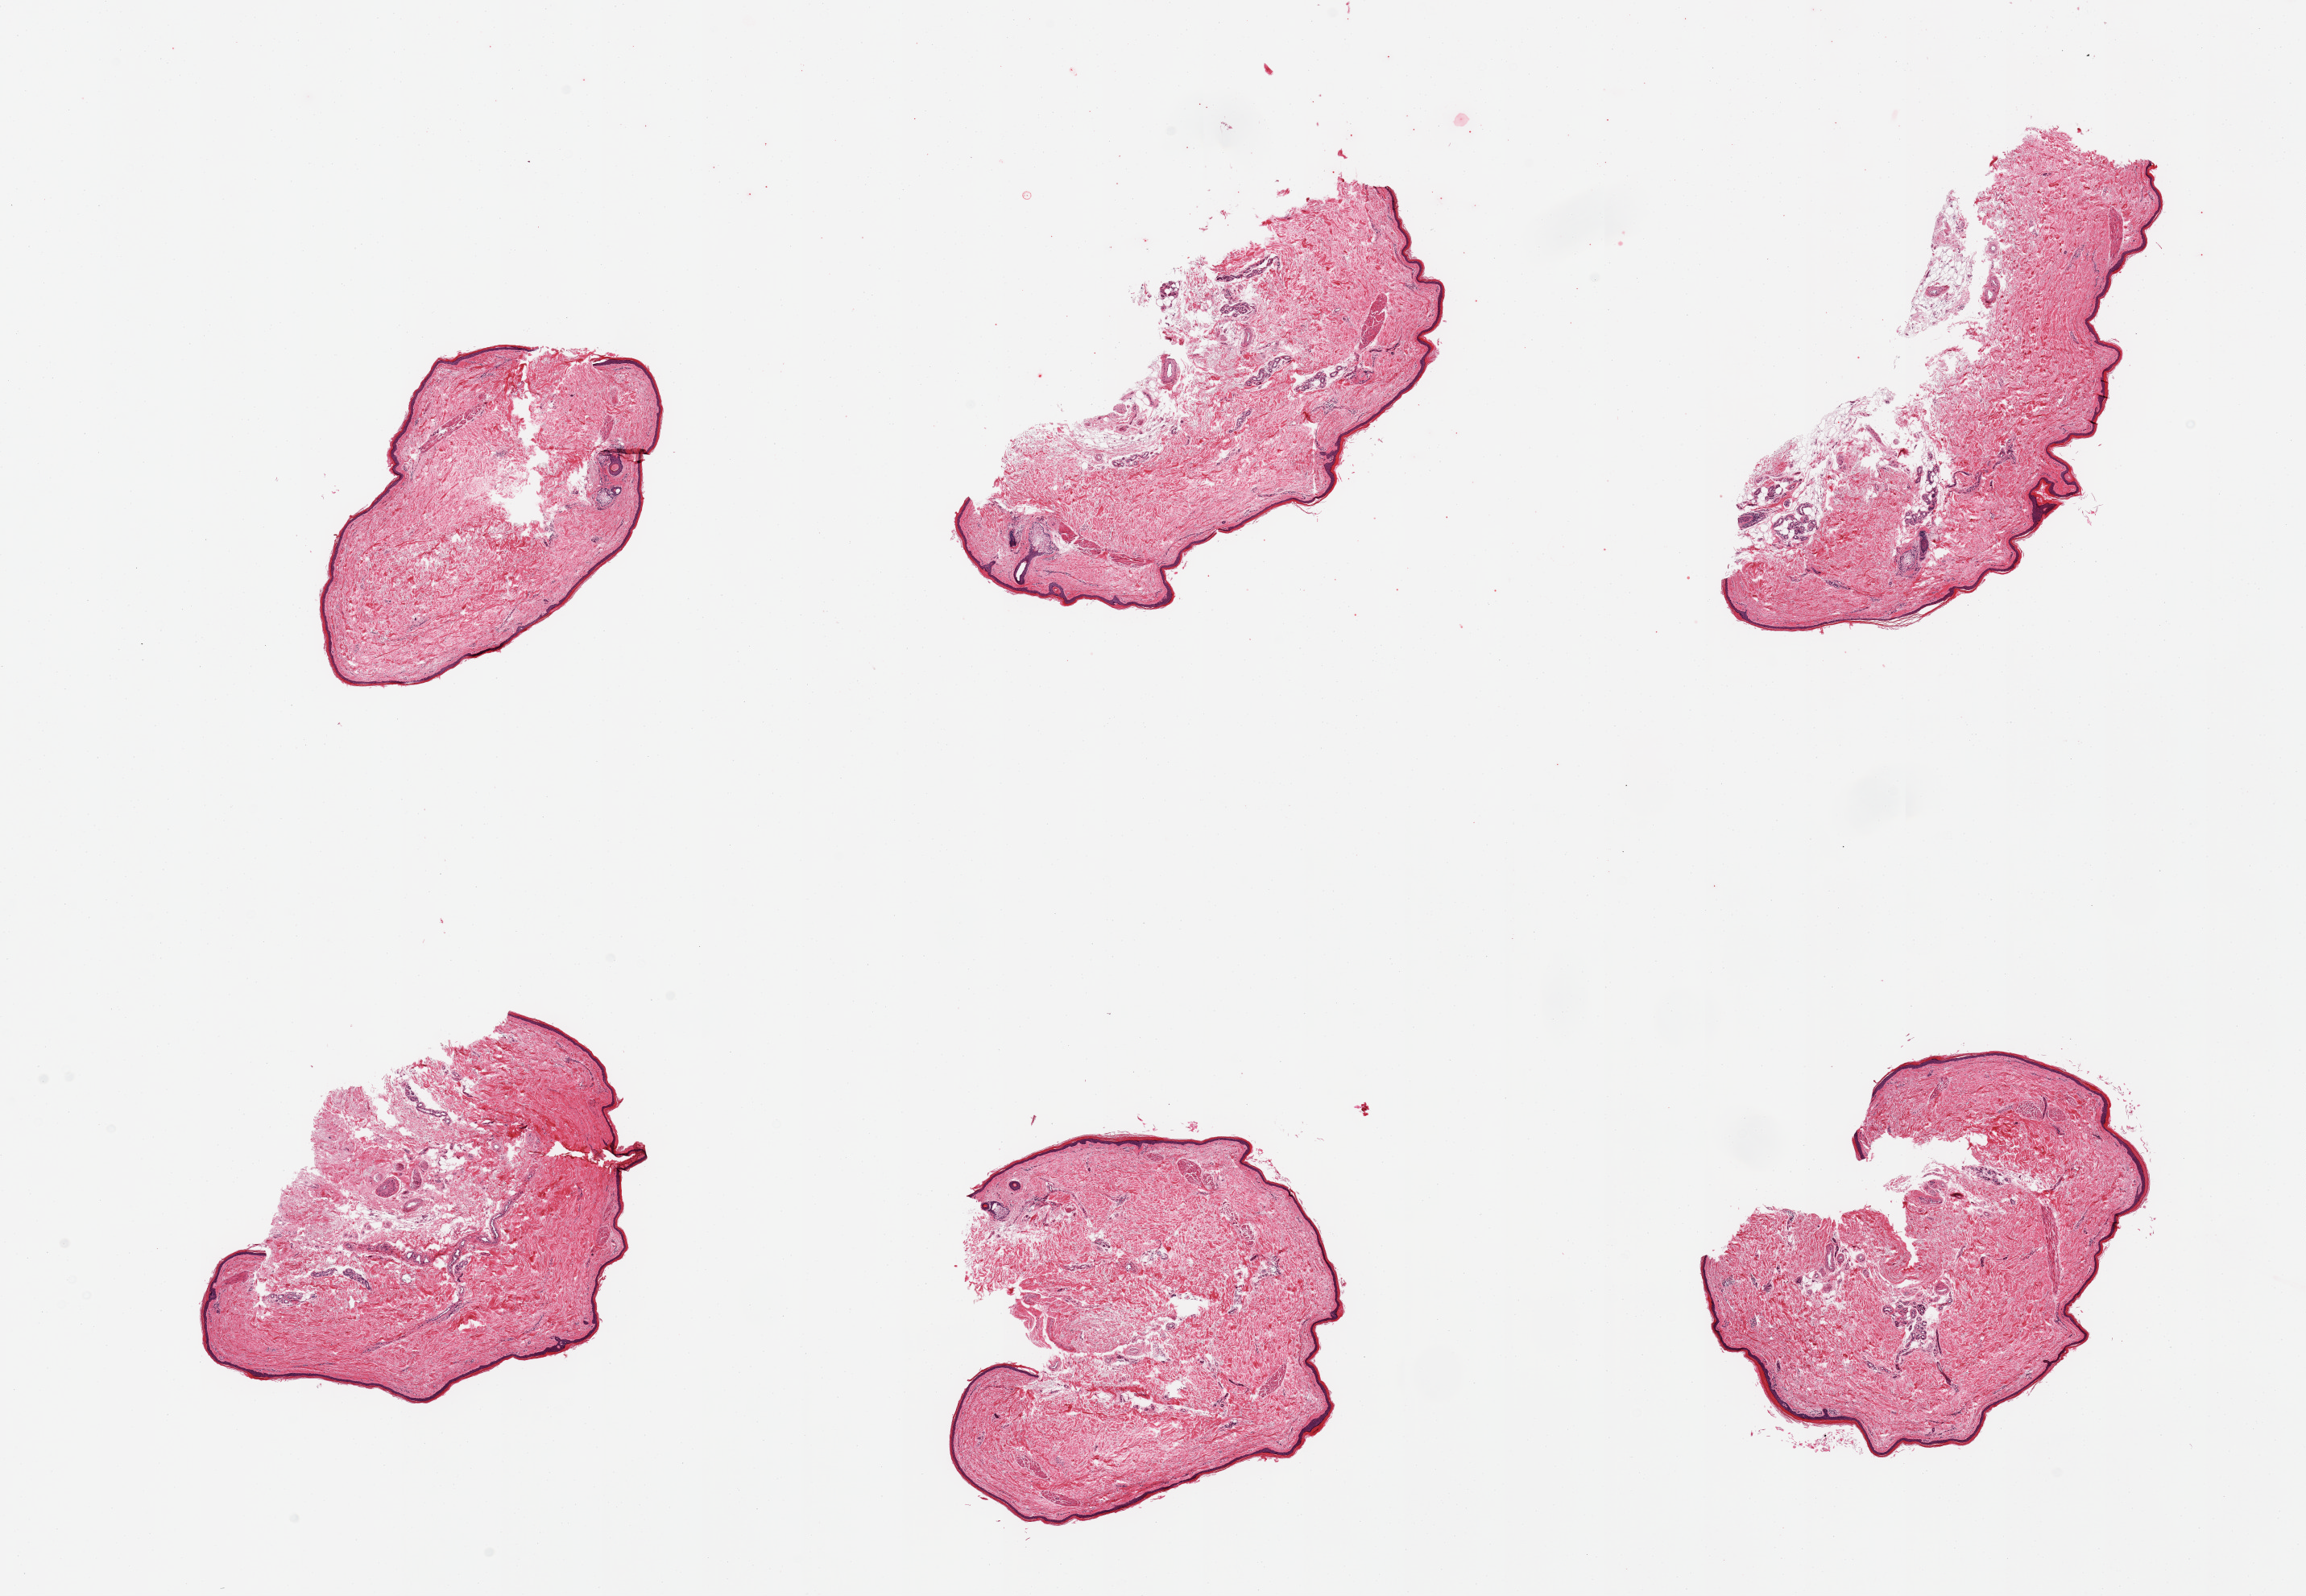
Whole-slide image, H&E stain, whole scanned area (about 22.6 x 15.7 mm) shown as a low-resolution overview, PAXgene-fixed, paraffin-embedded tissue, target tissue: skin of lower leg, donor tissue sample. Donor sex: male.
Review note (as recorded): 6 pieces, trace adherent dermal fat; squamous epithelium is ~30-40 microns.